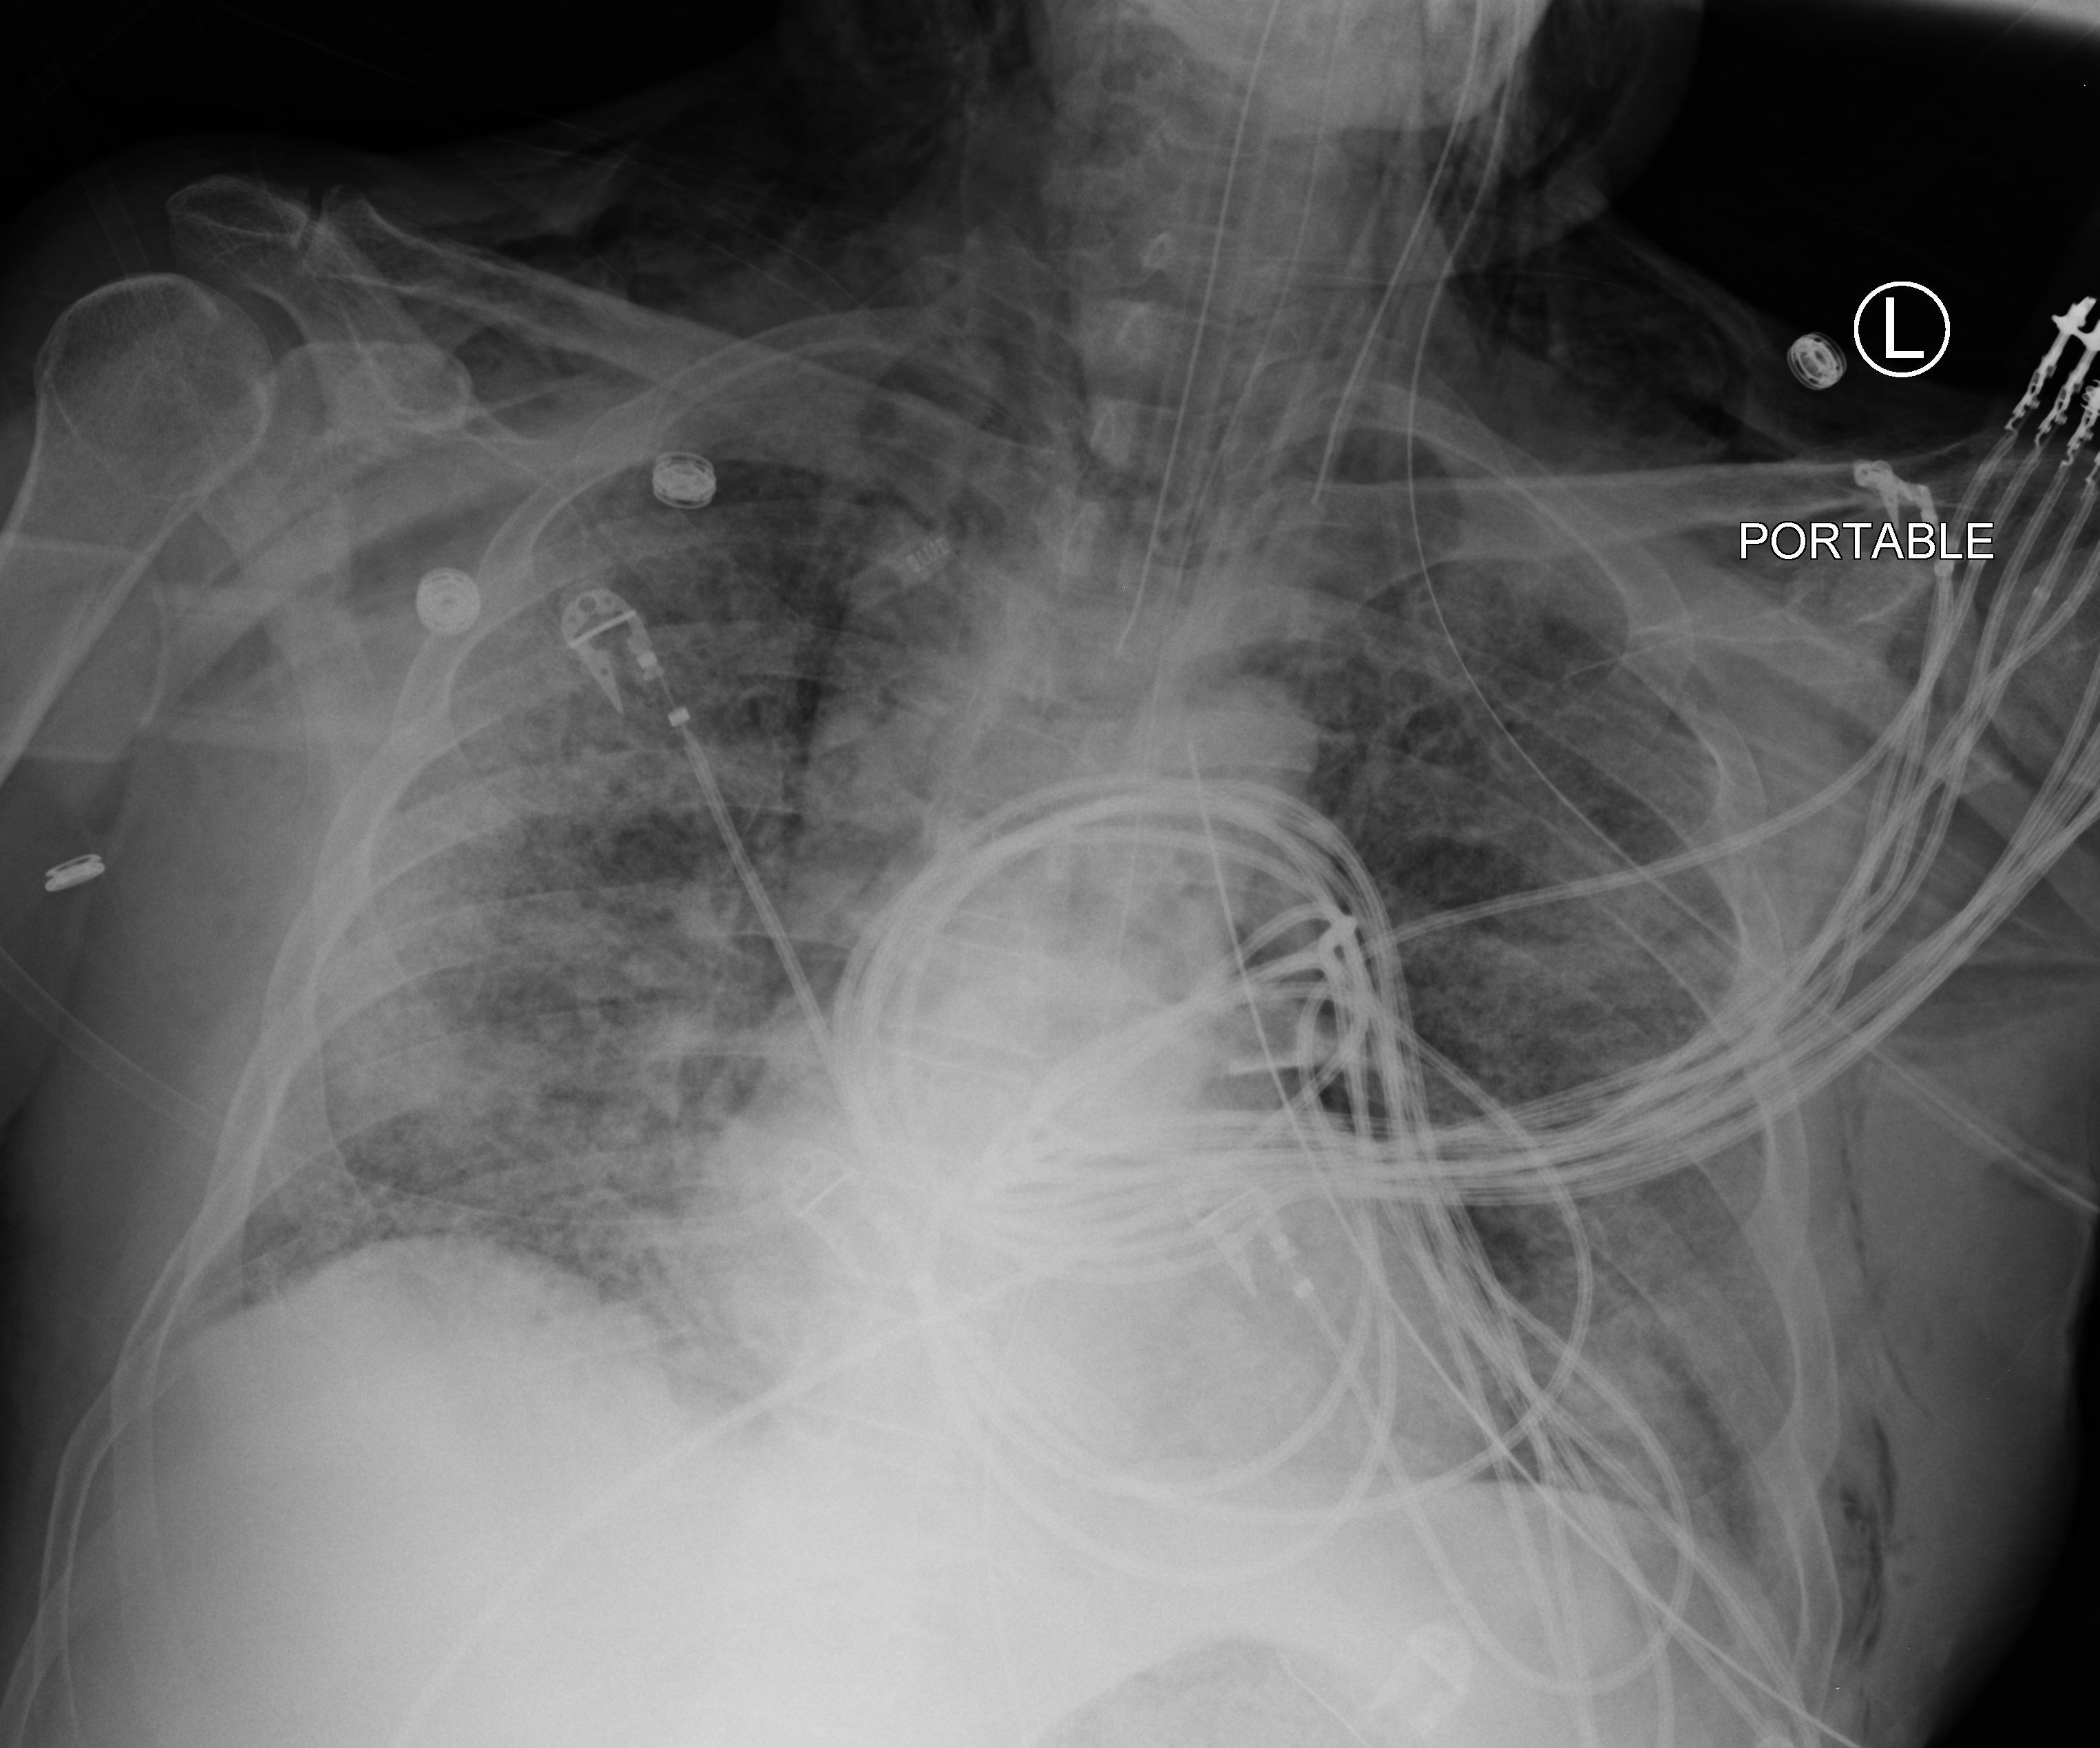
Portable chest radiograph. Male patient hospitalised with COVID-19, age 60–74 years.
Admission-level facts for this patient (not findings on this image; timing relative to this image not recorded):
- mechanically ventilated during this hospital stay: yes
- admitted to intensive care during this hospital stay: yes